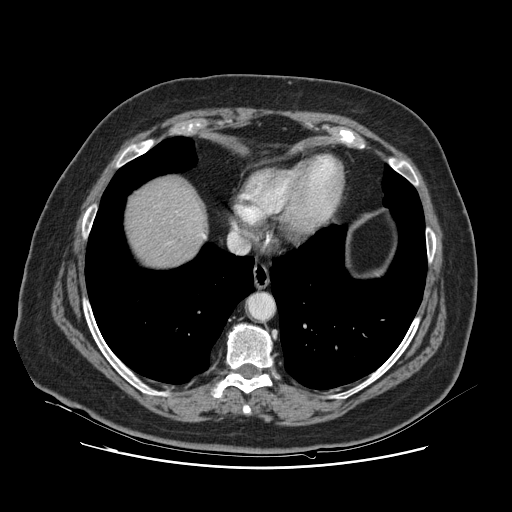
Contrast-enhanced abdominal CT, one axial slice; slice 115 of 132 in the series (ordered by position); intravenous contrast given; soft-tissue window (W 400 / L 40 HU); 2.5 mm slice thickness; 512 × 512 image matrix, field of view 391 × 391 mm. Female patient, age 73 years. Case-level facts recorded for this patient, not image findings: diagnosis: colorectal cancer liver metastases, imaged before liver resection; multiple liver metastases: no; largest metastasis: 7 cm; chemotherapy before resection: yes.
Outlined on this slice (outlined manually by an expert reader):
- liver: bounding box (x1, y1, x2, y2) in pixels: (126, 178, 203, 266)
- planned liver remnant (the part of the liver to remain after resection): (126, 178, 203, 266)